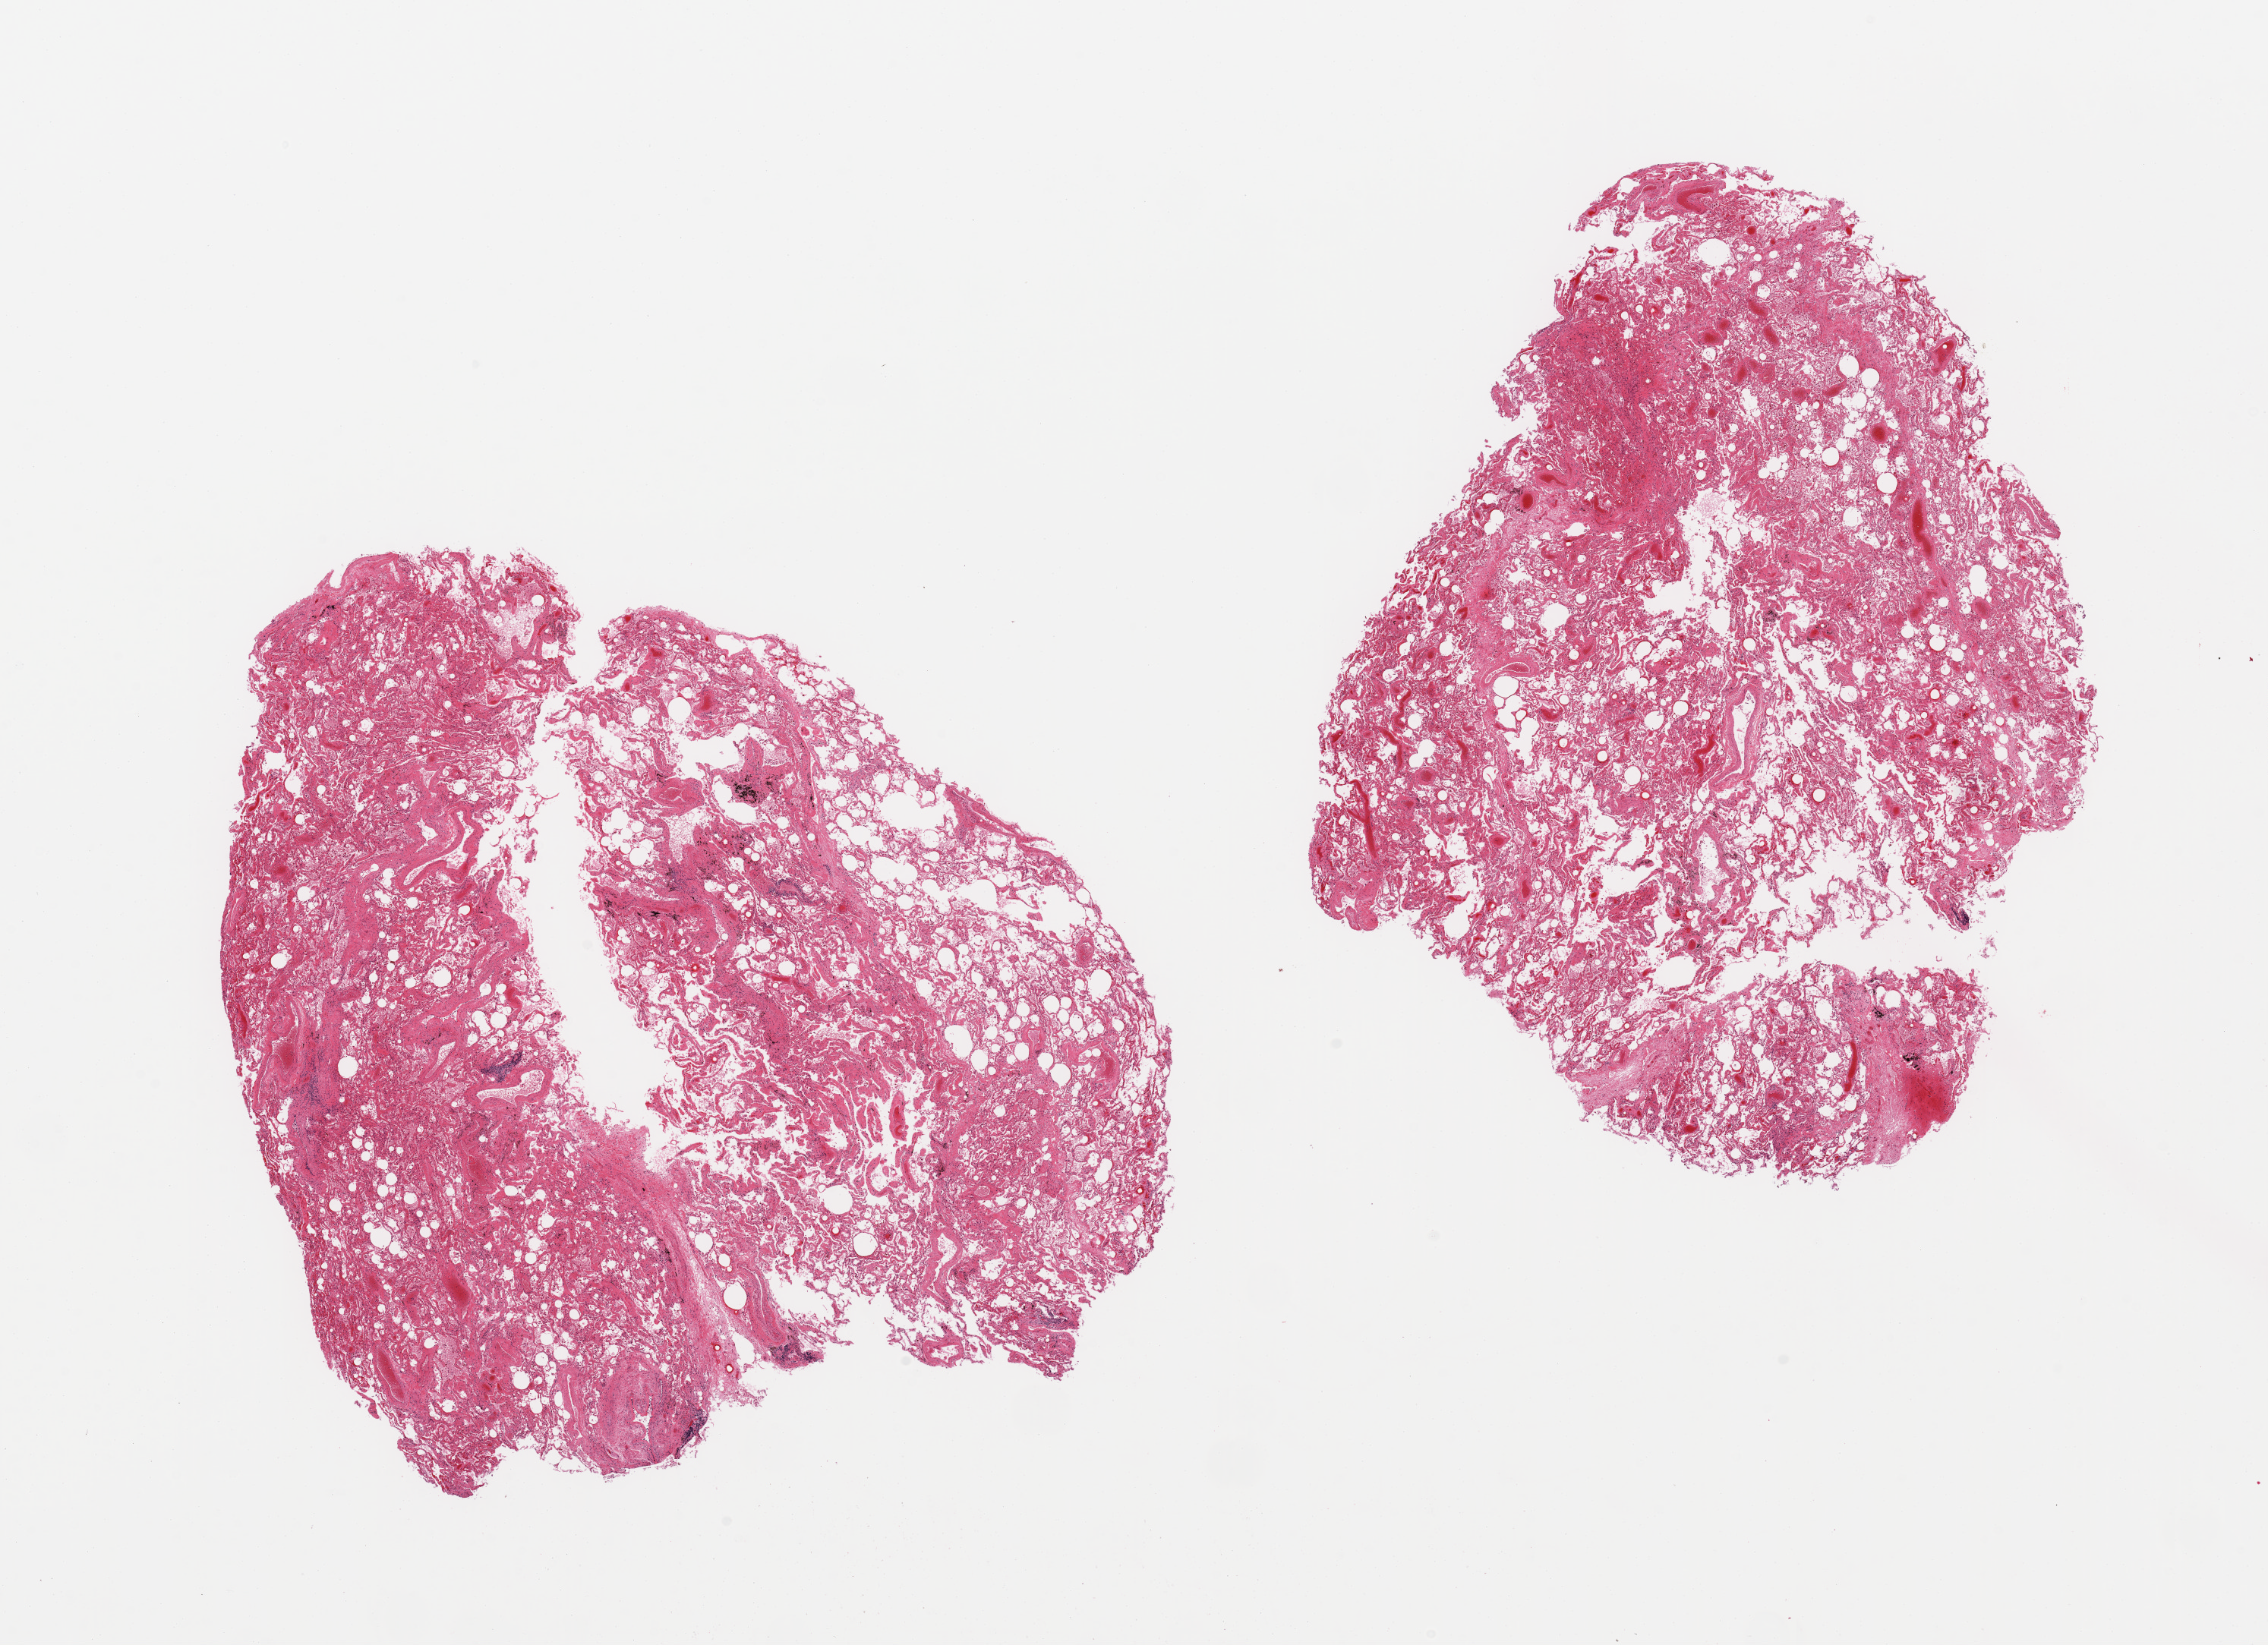
H&E whole-slide image, a low-resolution overview of the entire scanned area, about 23.6 x 17.1 mm (acquisition: 20x scan), PAXgene-fixed paraffin-embedded (PFPE) section, target tissue: lung, tissue donor sample.
Reviewer comment on this tissue sample: 2 pieces; patchy moderate interstitial fibrosis; moderate alveolar edema.